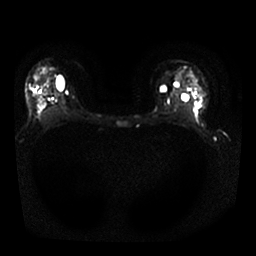
Breast MRI, one axial slice. Slice 18 of 25 in the series (ordered by position). Diffusion-weighted series; image 2 of 4 stored at this slice position (different b-values; order by instance number). 1.5 T. 4 mm slice thickness. 256 × 256 image matrix, field of view 330 × 330 mm. Female patient.
Structures marked on this image (outlined manually by an expert reader):
- tumour on diffusion-weighted imaging: box from (x=38, y=65) to (x=50, y=121) px